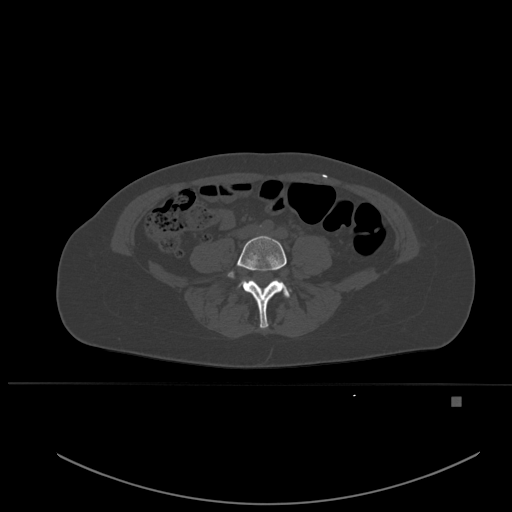
CT including the spine, one axial slice; position 170 of 651 along the scan axis; bone window (W 1800 / L 400 HU); 1.5 mm slice thickness; 512 × 512 image matrix, field of view 443 × 443 mm. Female patient, age 49 years. From the clinical record (not read from this slice): primary cancer: breast.
Outlined on this slice (semi-automatically segmented with operator editing):
- L4 vertebra: bounding box (x1, y1, x2, y2) in pixels: (227, 235, 289, 329)
- L5 vertebra: (241, 282, 243, 286)